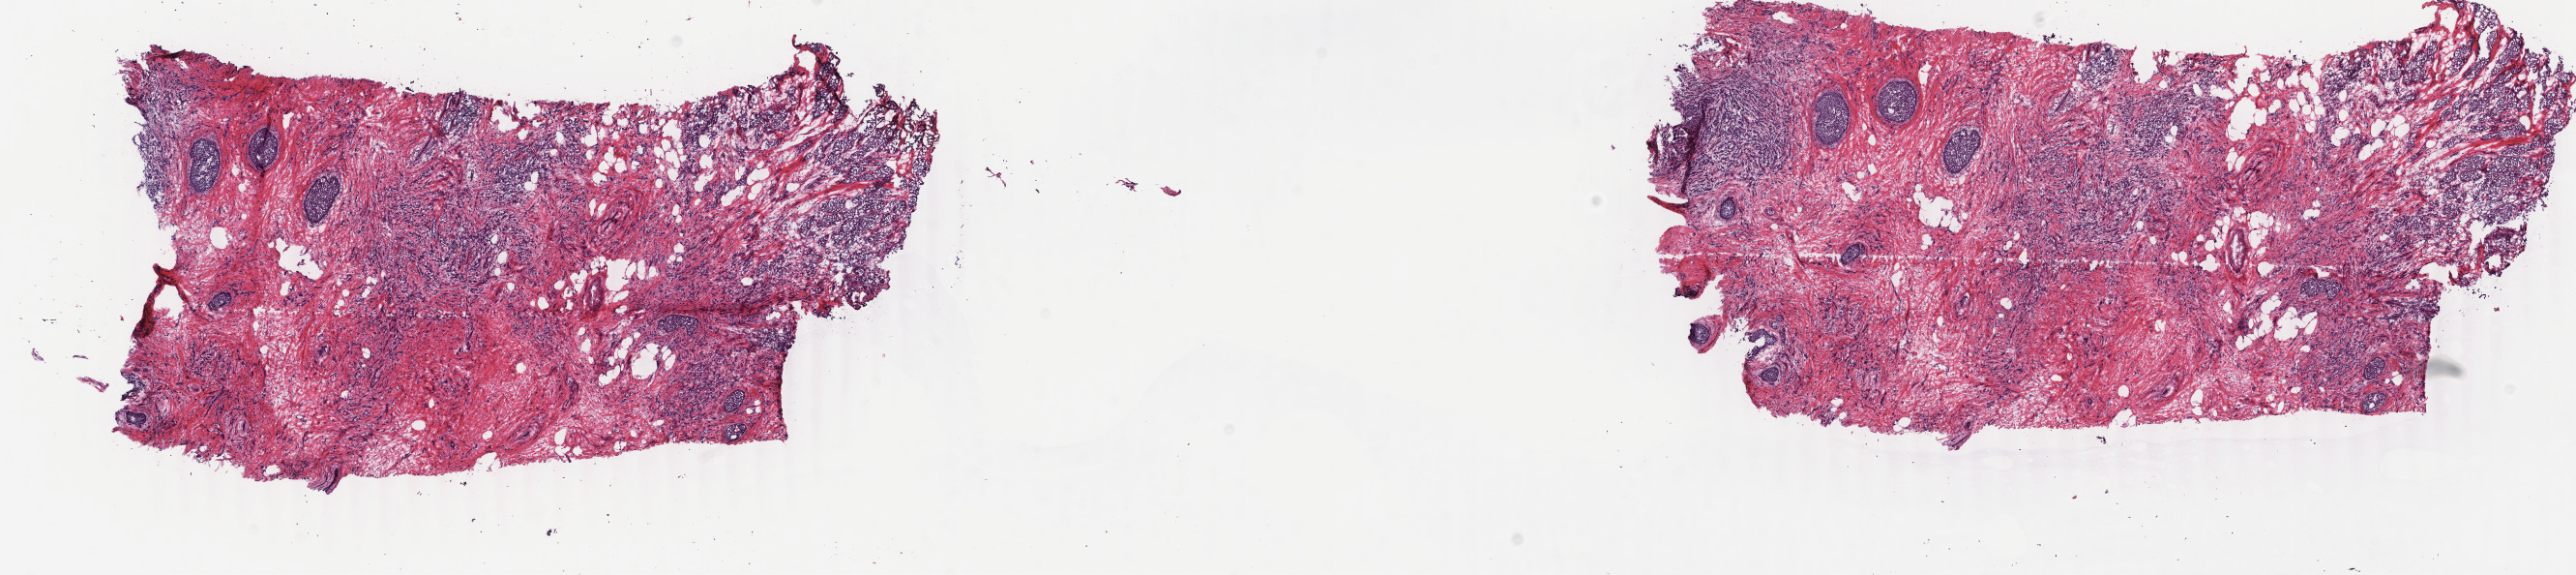
Digitized H&E tissue section (whole slide), whole scanned area (about 21.2 x 4.7 mm) shown as a low-resolution overview, frozen section from the bottom of the tissue portion, primary tumour sample from the breast. Patient: female, age at initial diagnosis 62 years.
Pathologic diagnosis: Infiltrating duct and lobular carcinoma.